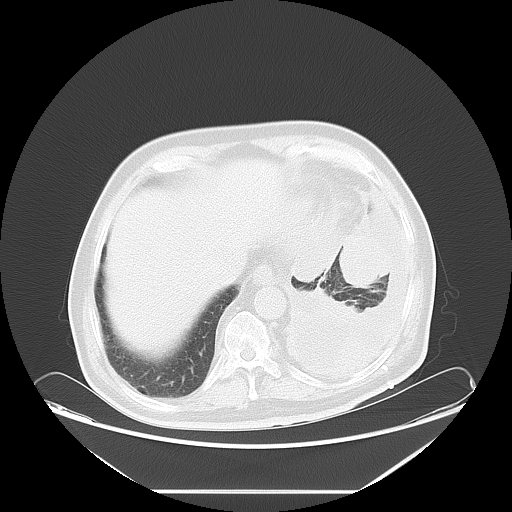
Chest CT, one axial slice. Slice 16 of 63 in the series (ordered by position). Reconstruction kernel LUNG. 120 kVp. Lung window (W 1500 / L -600 HU). 5 mm slice thickness. 512 × 512 image matrix. Male patient, age 67 years. Case-level facts recorded for this patient, not image findings: clinical TNM (as recorded): T1b N1 M1a; histopathological grade: G3.
Annotated regions visible in this slice (rectangle marked by the reading radiologist):
- lung tumour (recorded histology: small cell carcinoma): bounding box (x1, y1, x2, y2) in pixels: (335, 229, 395, 292)